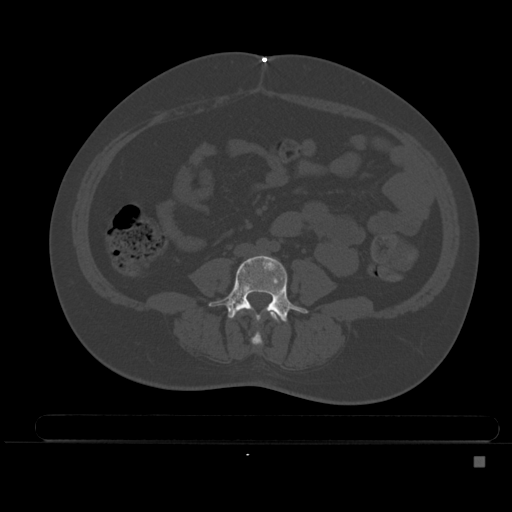
CT including the spine, one axial slice; bone window (W 1800 / L 400 HU); 1.5 mm slice thickness; 512 × 512 image matrix, field of view 404 × 404 mm. Female patient, age 33 years. From the clinical record (not read from this slice): primary cancer: breast.
Structures marked on this image (semi-automatically segmented with operator editing):
- L3 vertebra: box from (x=238, y=309) to (x=282, y=346) px
- L4 vertebra: (x=209, y=255)–(x=307, y=323)